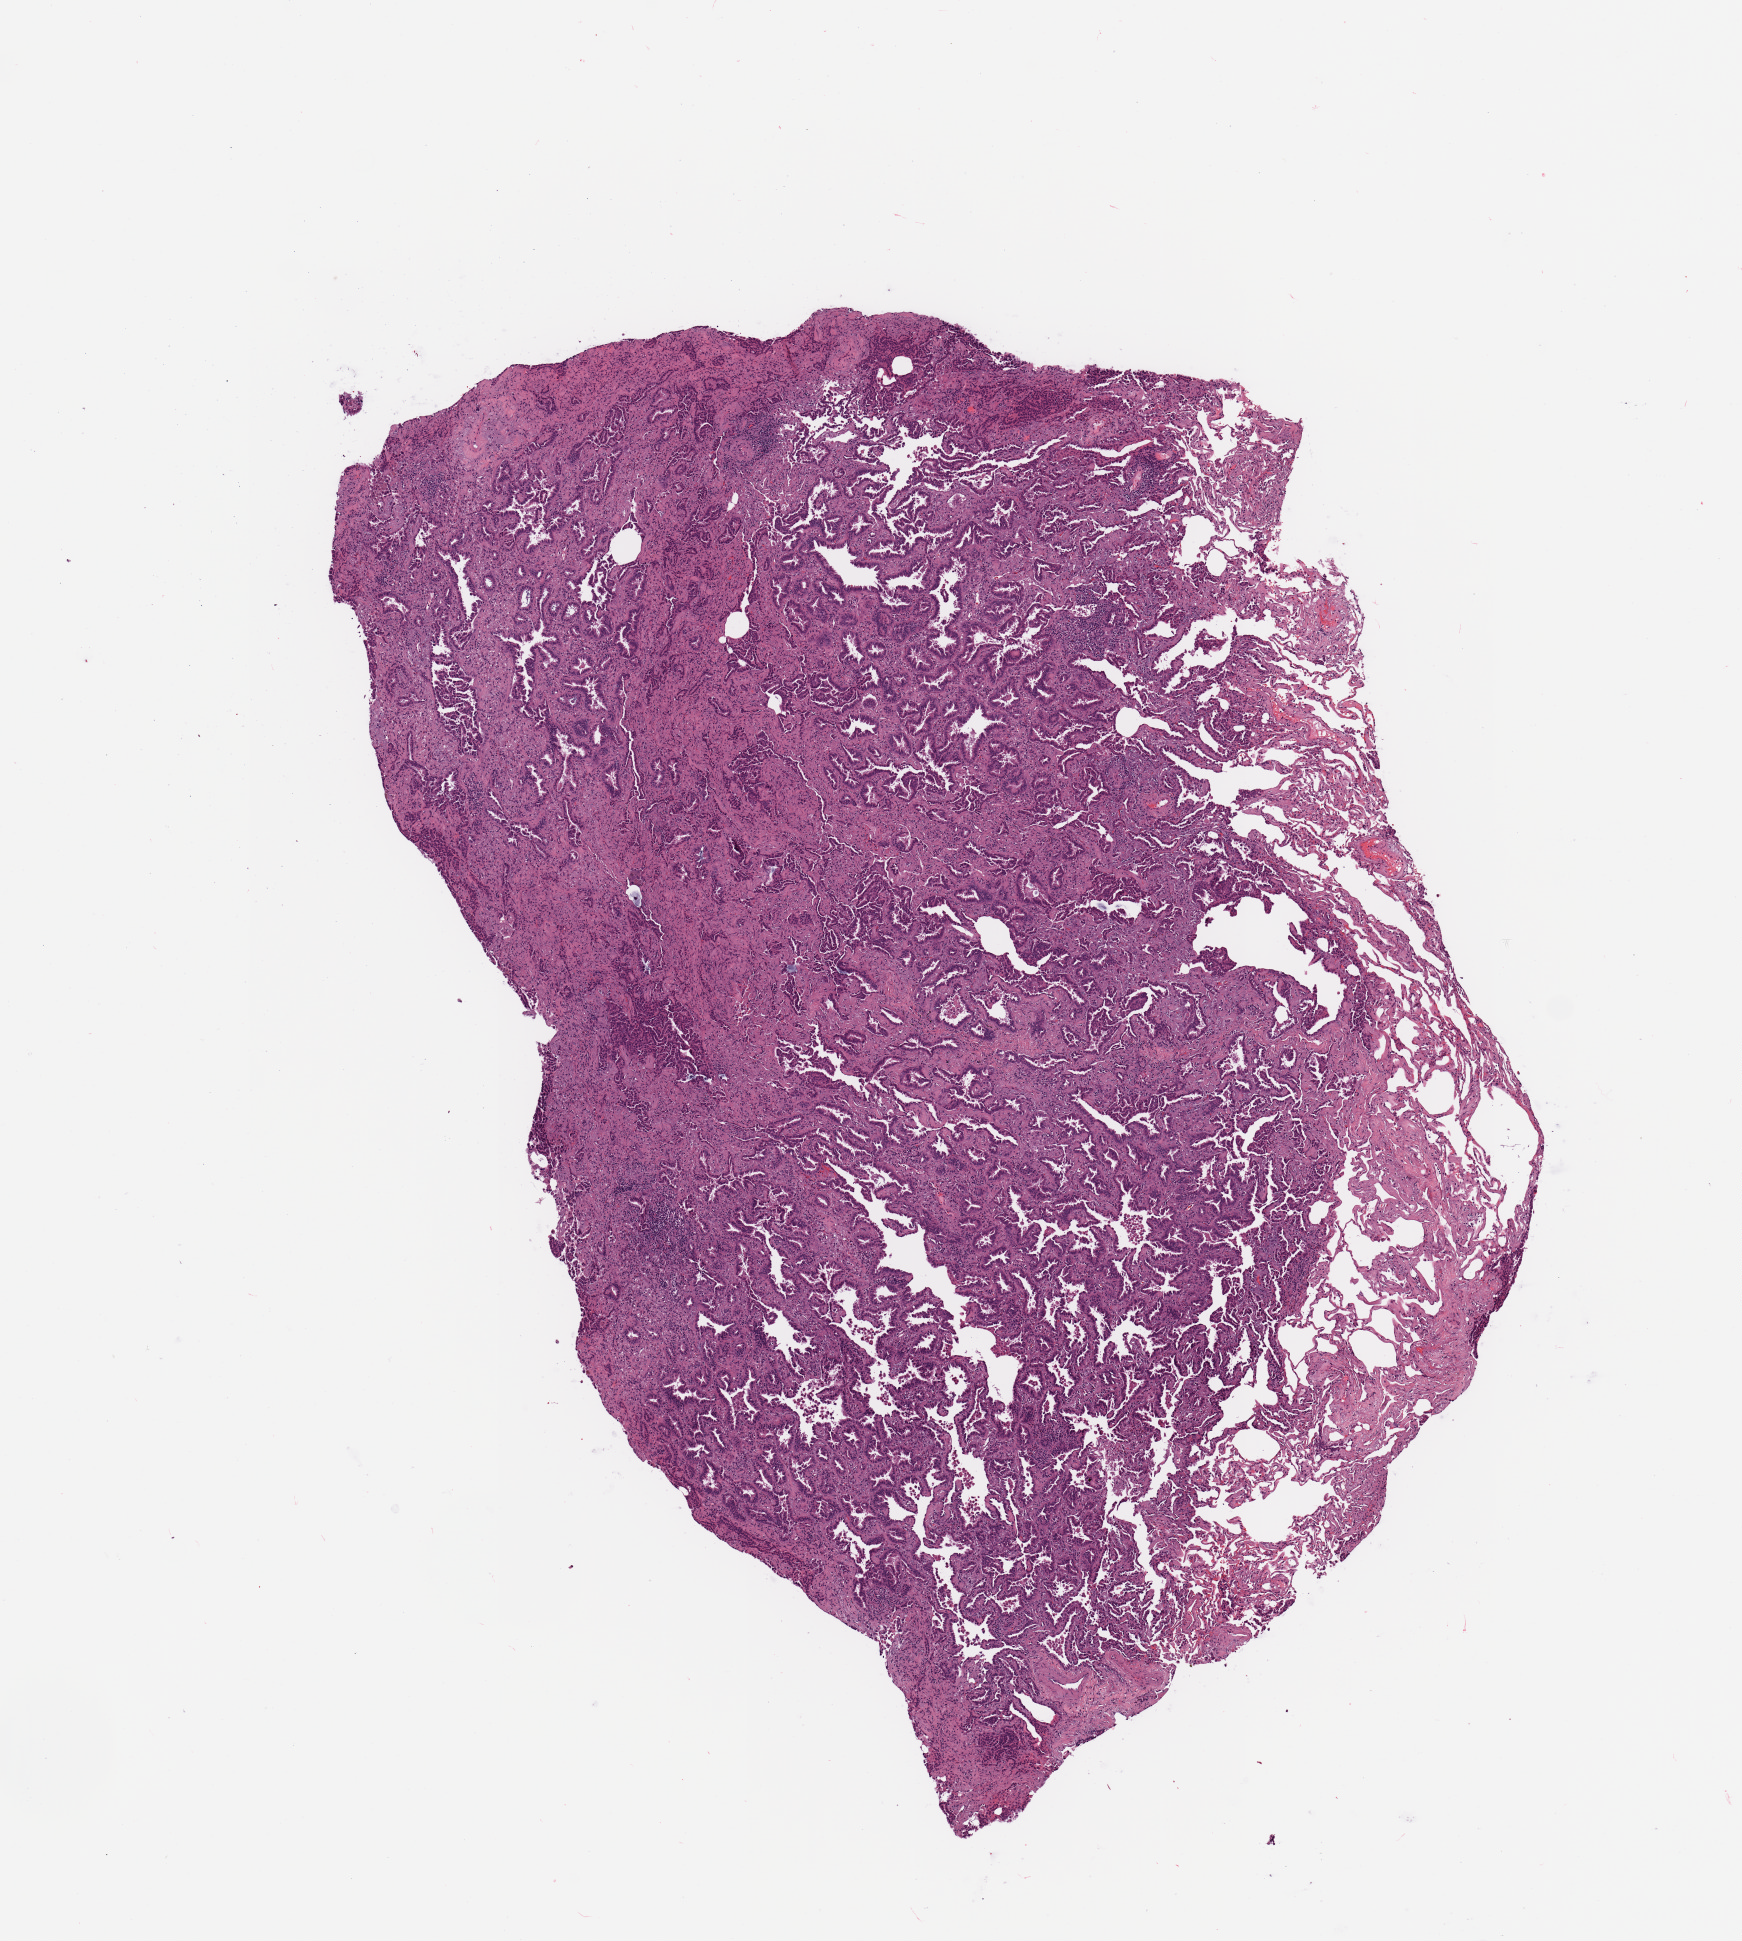
H&E whole-slide image, whole scanned area (about 6.9 x 7.7 mm, acquisition: 20x scan) shown as a low-resolution overview; tumour tissue sample, sampled site: lung. Female, 68 y/o. Histologic grade: G2 (moderately differentiated). Composition of this section per pathologist review: tumour nuclei 65%, necrosis 2%.
AJCC pathologic stage: IA. Primary tumour site (as recorded): left upper lobe. Diagnosis: Adenocarcinoma, NOS.